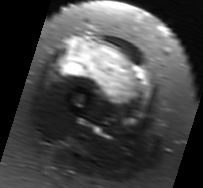
MRI of an extremity soft-tissue mass, one axial slice; position 25 of 91 along the scan axis; T2-weighted fat-saturated; MR volume resampled by the dataset authors to the PET/CT grid (not the native acquisition matrix); 3.27 mm slice thickness; 203 × 188 image matrix. Female patient. From the clinical record (not read from this slice): histological type: malignant solitary fibrous tumor; grade: intermediate; site of the primary tumour: right thigh.
Outlined on this slice (expert contour drawn on MRI and transferred to this co-registered scan by the dataset authors):
- gross tumour volume including surrounding oedema: bounding box <56,35,153,107> (left, top, right, bottom; pixels)
- gross tumour volume (mass): <63,46,134,98>